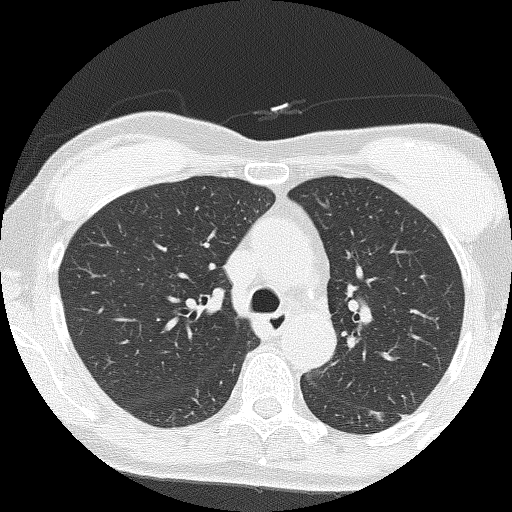
Low-dose screening chest CT, axial slice; second screening round (one year after baseline); lung window (W 1500 / L -600 HU); 2 mm slice thickness; lung (sharp) reconstruction kernel (FC51); 120 kVp; slice 52 of 159 in the series. Female, age 64 years at enrolment. Former smoker at enrolment.
• Lesion marked by an expert reader, bounding box [x1, y1, x2, y2] px = [352, 395, 412, 441].
• The screening reader recorded 3 non-calcified nodules or masses ≥4 mm on this exam; which of them this box marks is not recorded.
• Official screen result: positive, other.
• Participant outcome: lung cancer diagnosed 576 days after this screen (after the third annual screen) — adenocarcinoma, NOS, left lower lobe, moderately differentiated (G2), stage IA (AJCC 6th edition), 17 mm at pathology.